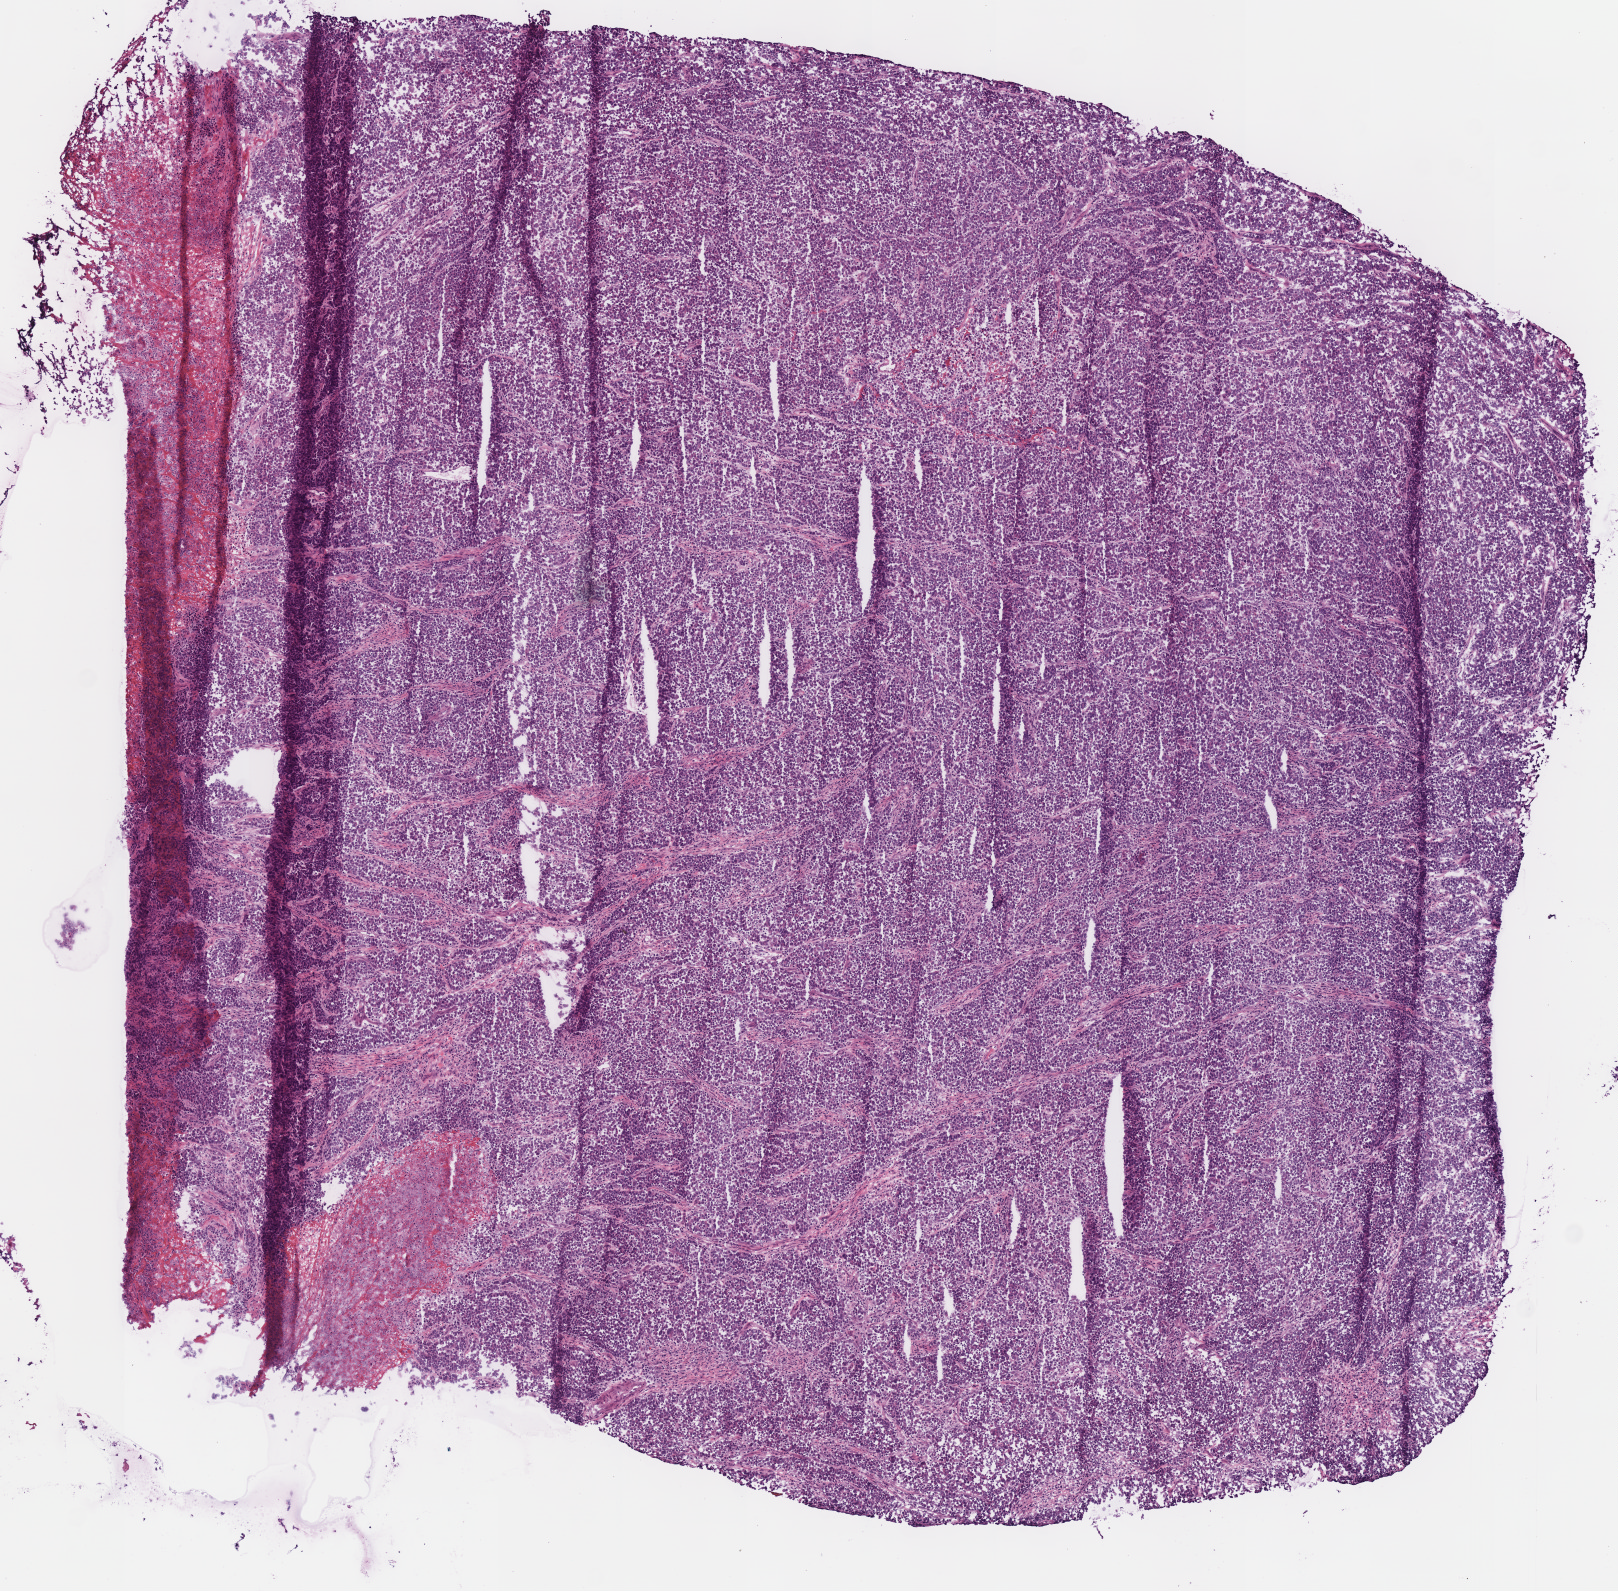
Whole-slide histology image, H&E — low-resolution overview of the scanned area, about 6.4 x 6.3 mm. Frozen section from the bottom of the tissue portion. Primary tumour sample from the stomach. Female patient; age at initial diagnosis 58 years. Histologic grade: G3 (poorly differentiated). Composition of this section per pathologist review: tumour cells 100%, tumour nuclei 75%, normal cells 0%, stromal cells 0%, necrosis 0%.
* histologic diagnosis: Carcinoma, diffuse type (gastric antrum)
* TNM: T4a N0 M0
* AJCC pathologic stage: IIB